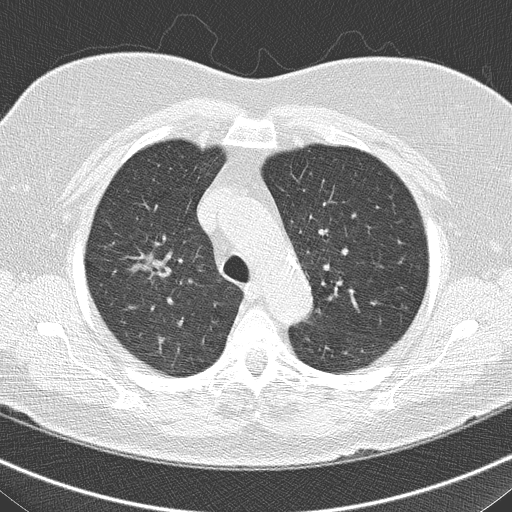
Chest CT (low-dose screening protocol), one axial image; third screening round (two years after baseline); lung window (W 1500 / L -600 HU). Female, age 74 years at enrolment. Former smoker at enrolment.
Expert-annotated lung lesion, bounding box (x1, y1, x2, y2) in pixels: (111, 237, 181, 299). The screening reader recorded 5 non-calcified nodules or masses ≥4 mm on this exam (right upper lobe, right middle lobe, right middle lobe, left lower lobe, right lower lobe); which of them this box marks is not recorded. Official screen result: positive, other. Lung cancer was diagnosed 117 days after this screen: bronchiolo-alveolar carcinoma, non-mucinous, right upper lobe, well differentiated (G1), stage IA (AJCC 6th edition), 14 mm at pathology.